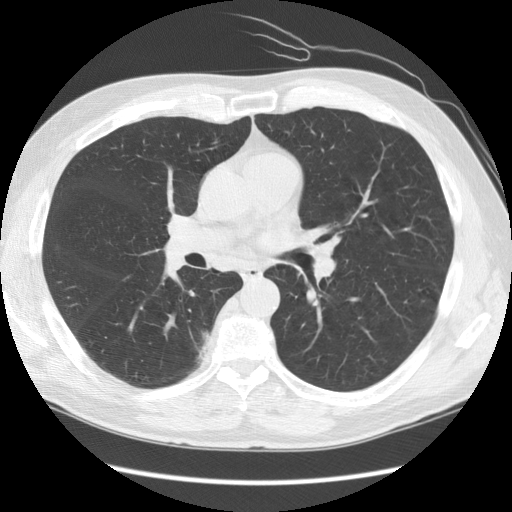
Low-dose screening chest CT, axial slice, first (baseline) screen, lung window (W 1500 / L -600 HU), standard (soft-tissue) reconstruction kernel (STANDARD), 120 kVp. Male participant, aged 69 years at enrolment.
Expert-annotated lung lesion, bounding box (x1, y1, x2, y2) in pixels: (169, 317, 228, 373). No non-calcified nodule or mass ≥4 mm was recorded by the screening reader at this exam. Official screen result: negative screen, minor abnormalities not suspicious for lung cancer. Participant outcome: lung cancer diagnosed 497 days after this screen — bronchiolo-alveolar adenocarcinoma, NOS, right lower lobe, well differentiated (G1), stage IB (AJCC 6th edition), 23 mm at pathology.